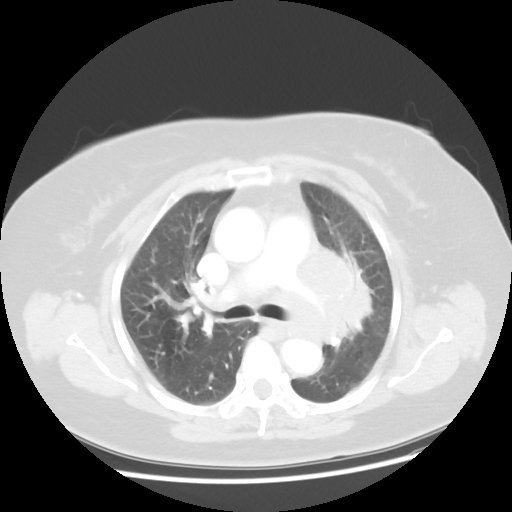
Chest CT, one axial slice. Position 29 of 49 along the scan axis. Reconstruction kernel STANDARD. 120 kVp. Lung window (W 1500 / L -600 HU). 5 mm slice thickness. 512 × 512 image matrix, field of view 374 × 374 mm. Female patient, age 58 years. From the clinical record (not read from this slice): clinical TNM (as recorded): T4 N3 M0.
Outlined on this slice (rectangle marked by the reading radiologist):
- lung tumour (recorded histology: small cell carcinoma): bounding box <269,230,381,381> (left, top, right, bottom; pixels)